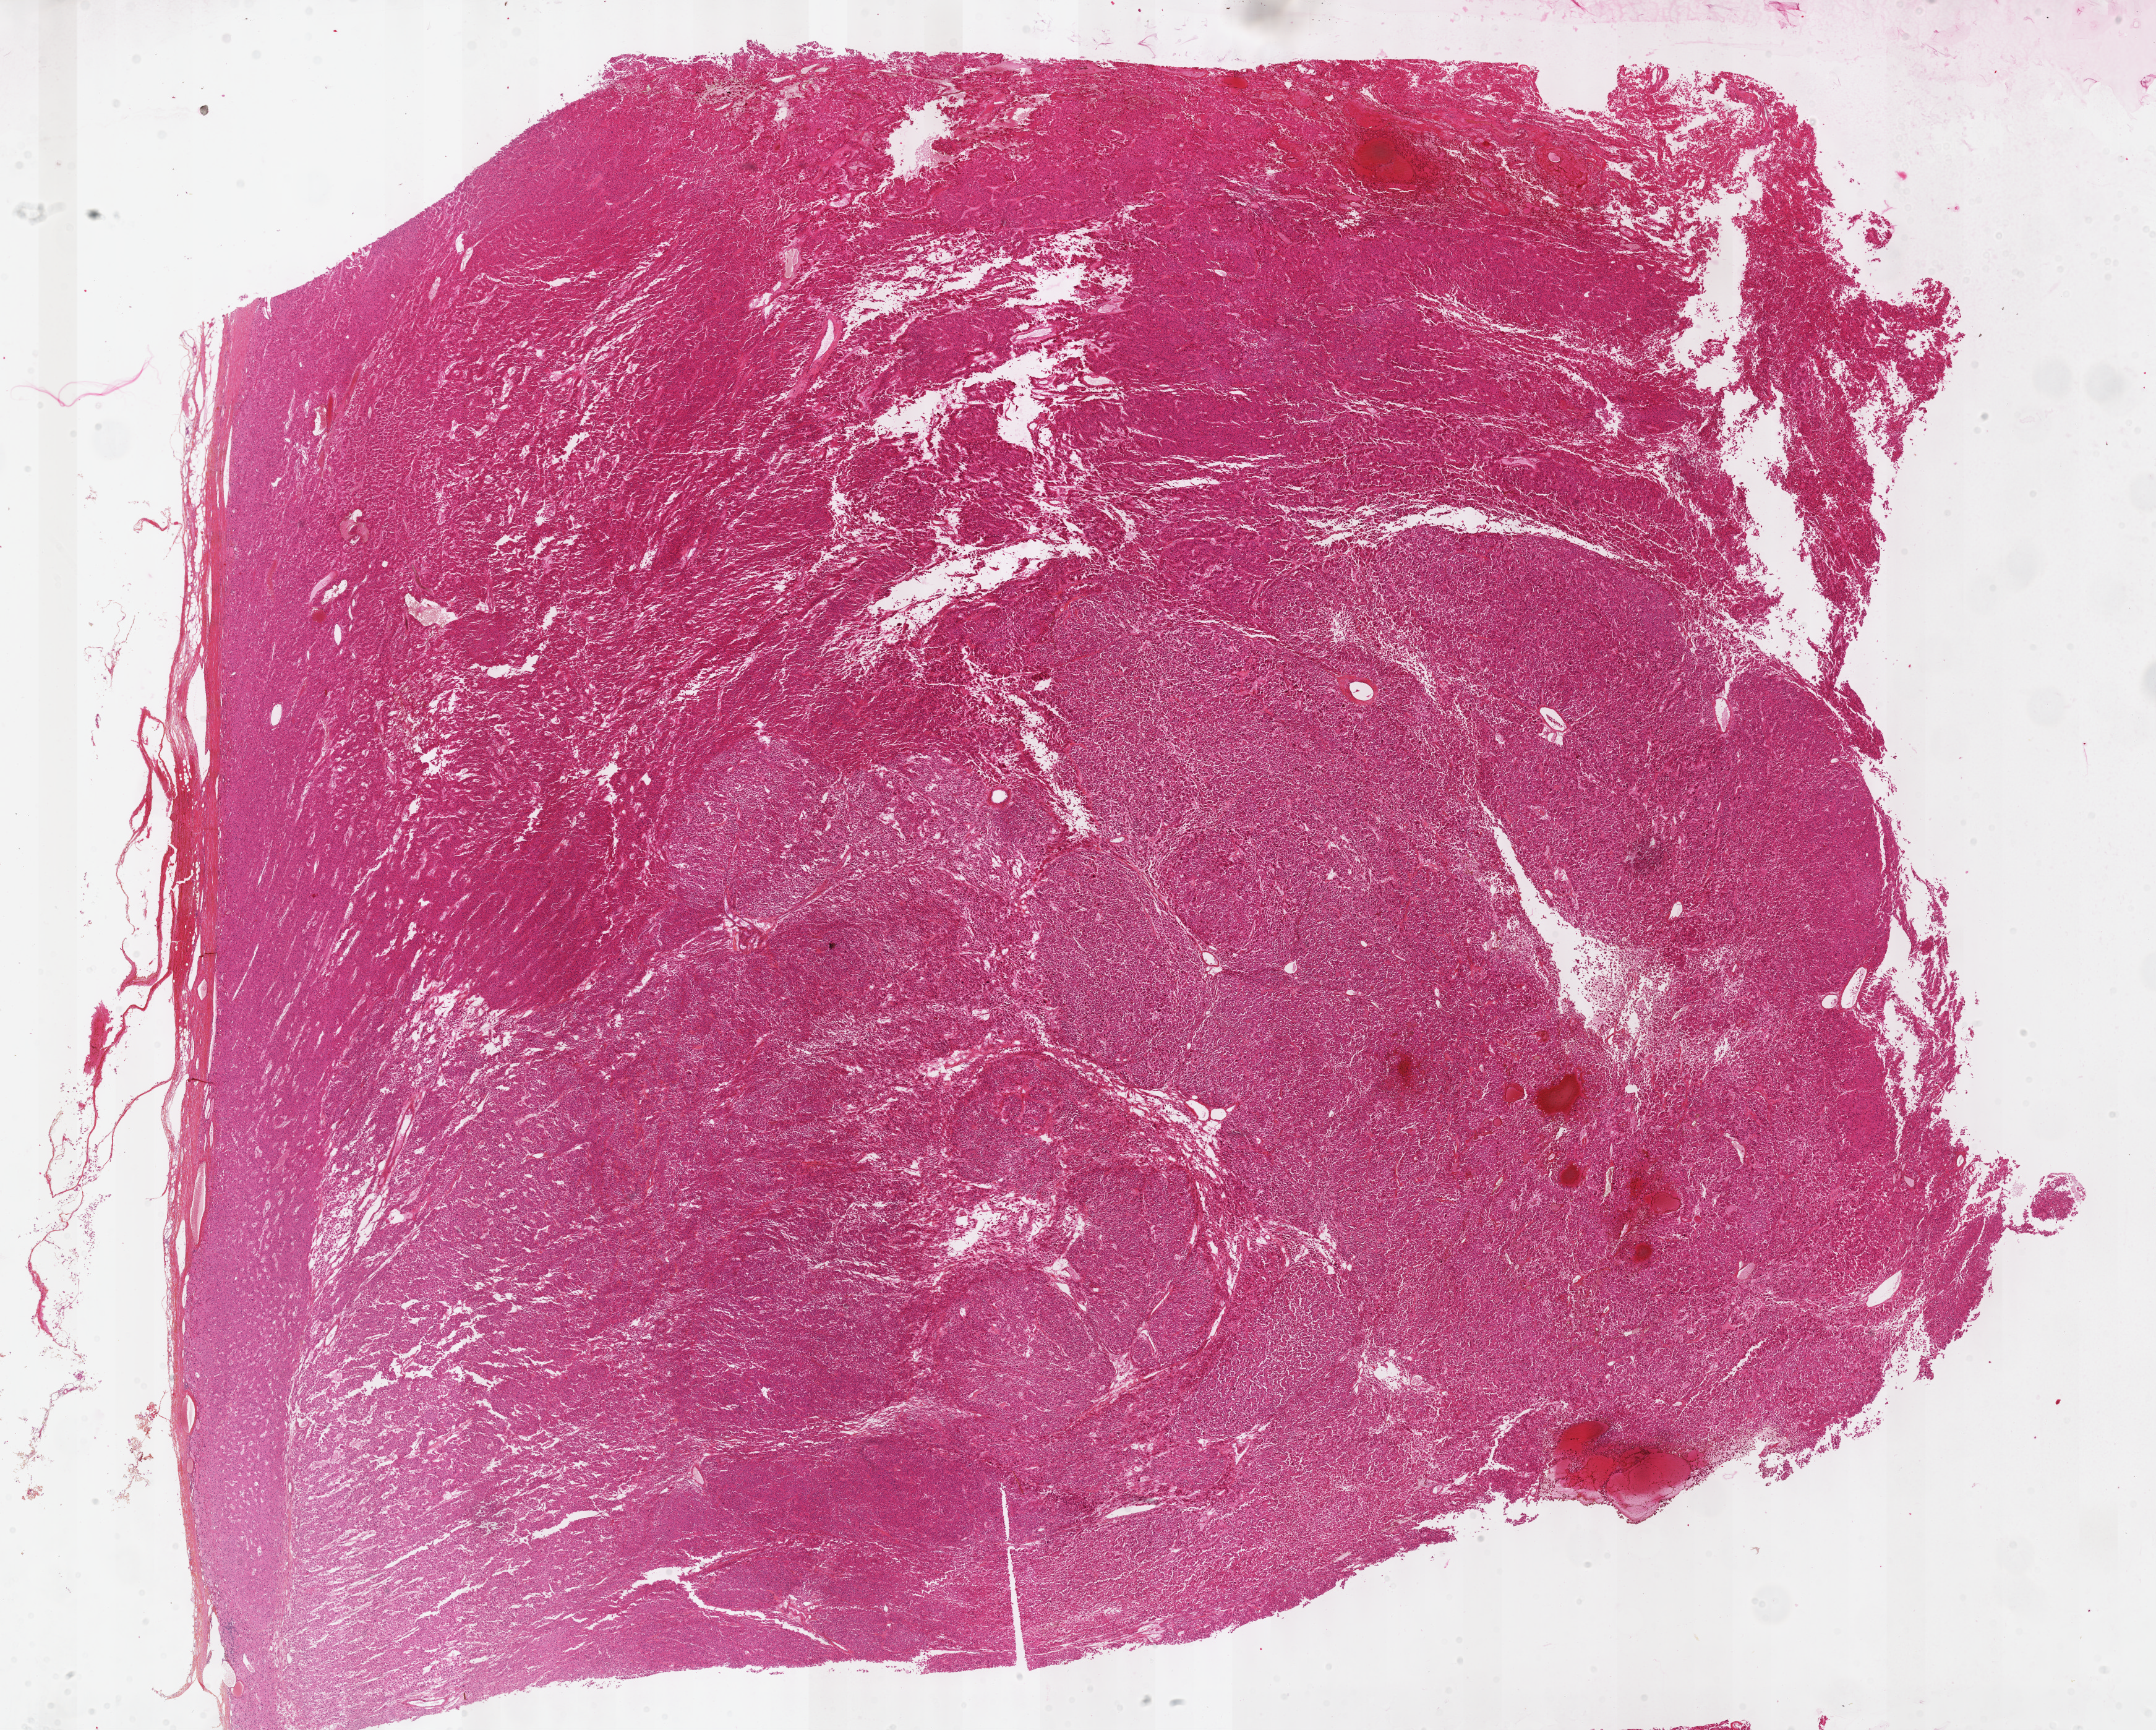
Digitized H&E tissue section (whole slide) — low-resolution overview of the scanned area, about 28.2 x 22.6 mm, formalin-fixed paraffin-embedded (FFPE) diagnostic section, primary tumour sample from the adrenal cortex. Patient: male, age at initial diagnosis 57 years.
Lymph nodes positive (case pathology): 0 of 18 examined. Pathologic diagnosis: Adrenal cortical carcinoma. Laterality: left.